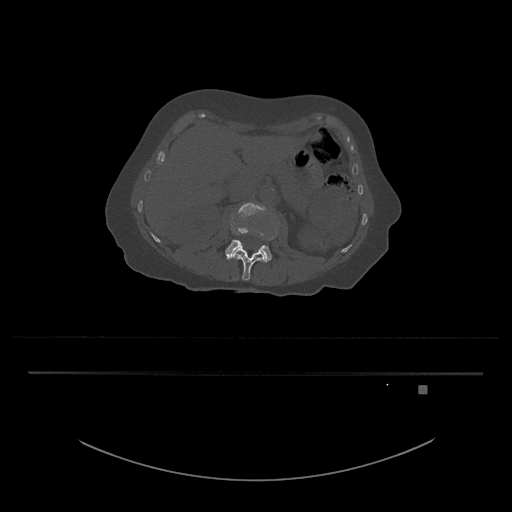
CT including the spine, one axial slice. Slice 462 of 797 in the series (ordered by position). Reconstruction kernel Br40s/3. Bone window (W 1800 / L 400 HU). 0.5 mm slice thickness. 512 × 512 image matrix, field of view 500 × 500 mm. Patient: female, 57 years. Case-level facts recorded for this patient, not image findings: primary cancer: cervical.
Outlined on this slice (semi-automatic segmentation, software-assisted and operator-edited):
- L3 vertebra: bounding box <225,202,278,262> (left, top, right, bottom; pixels)